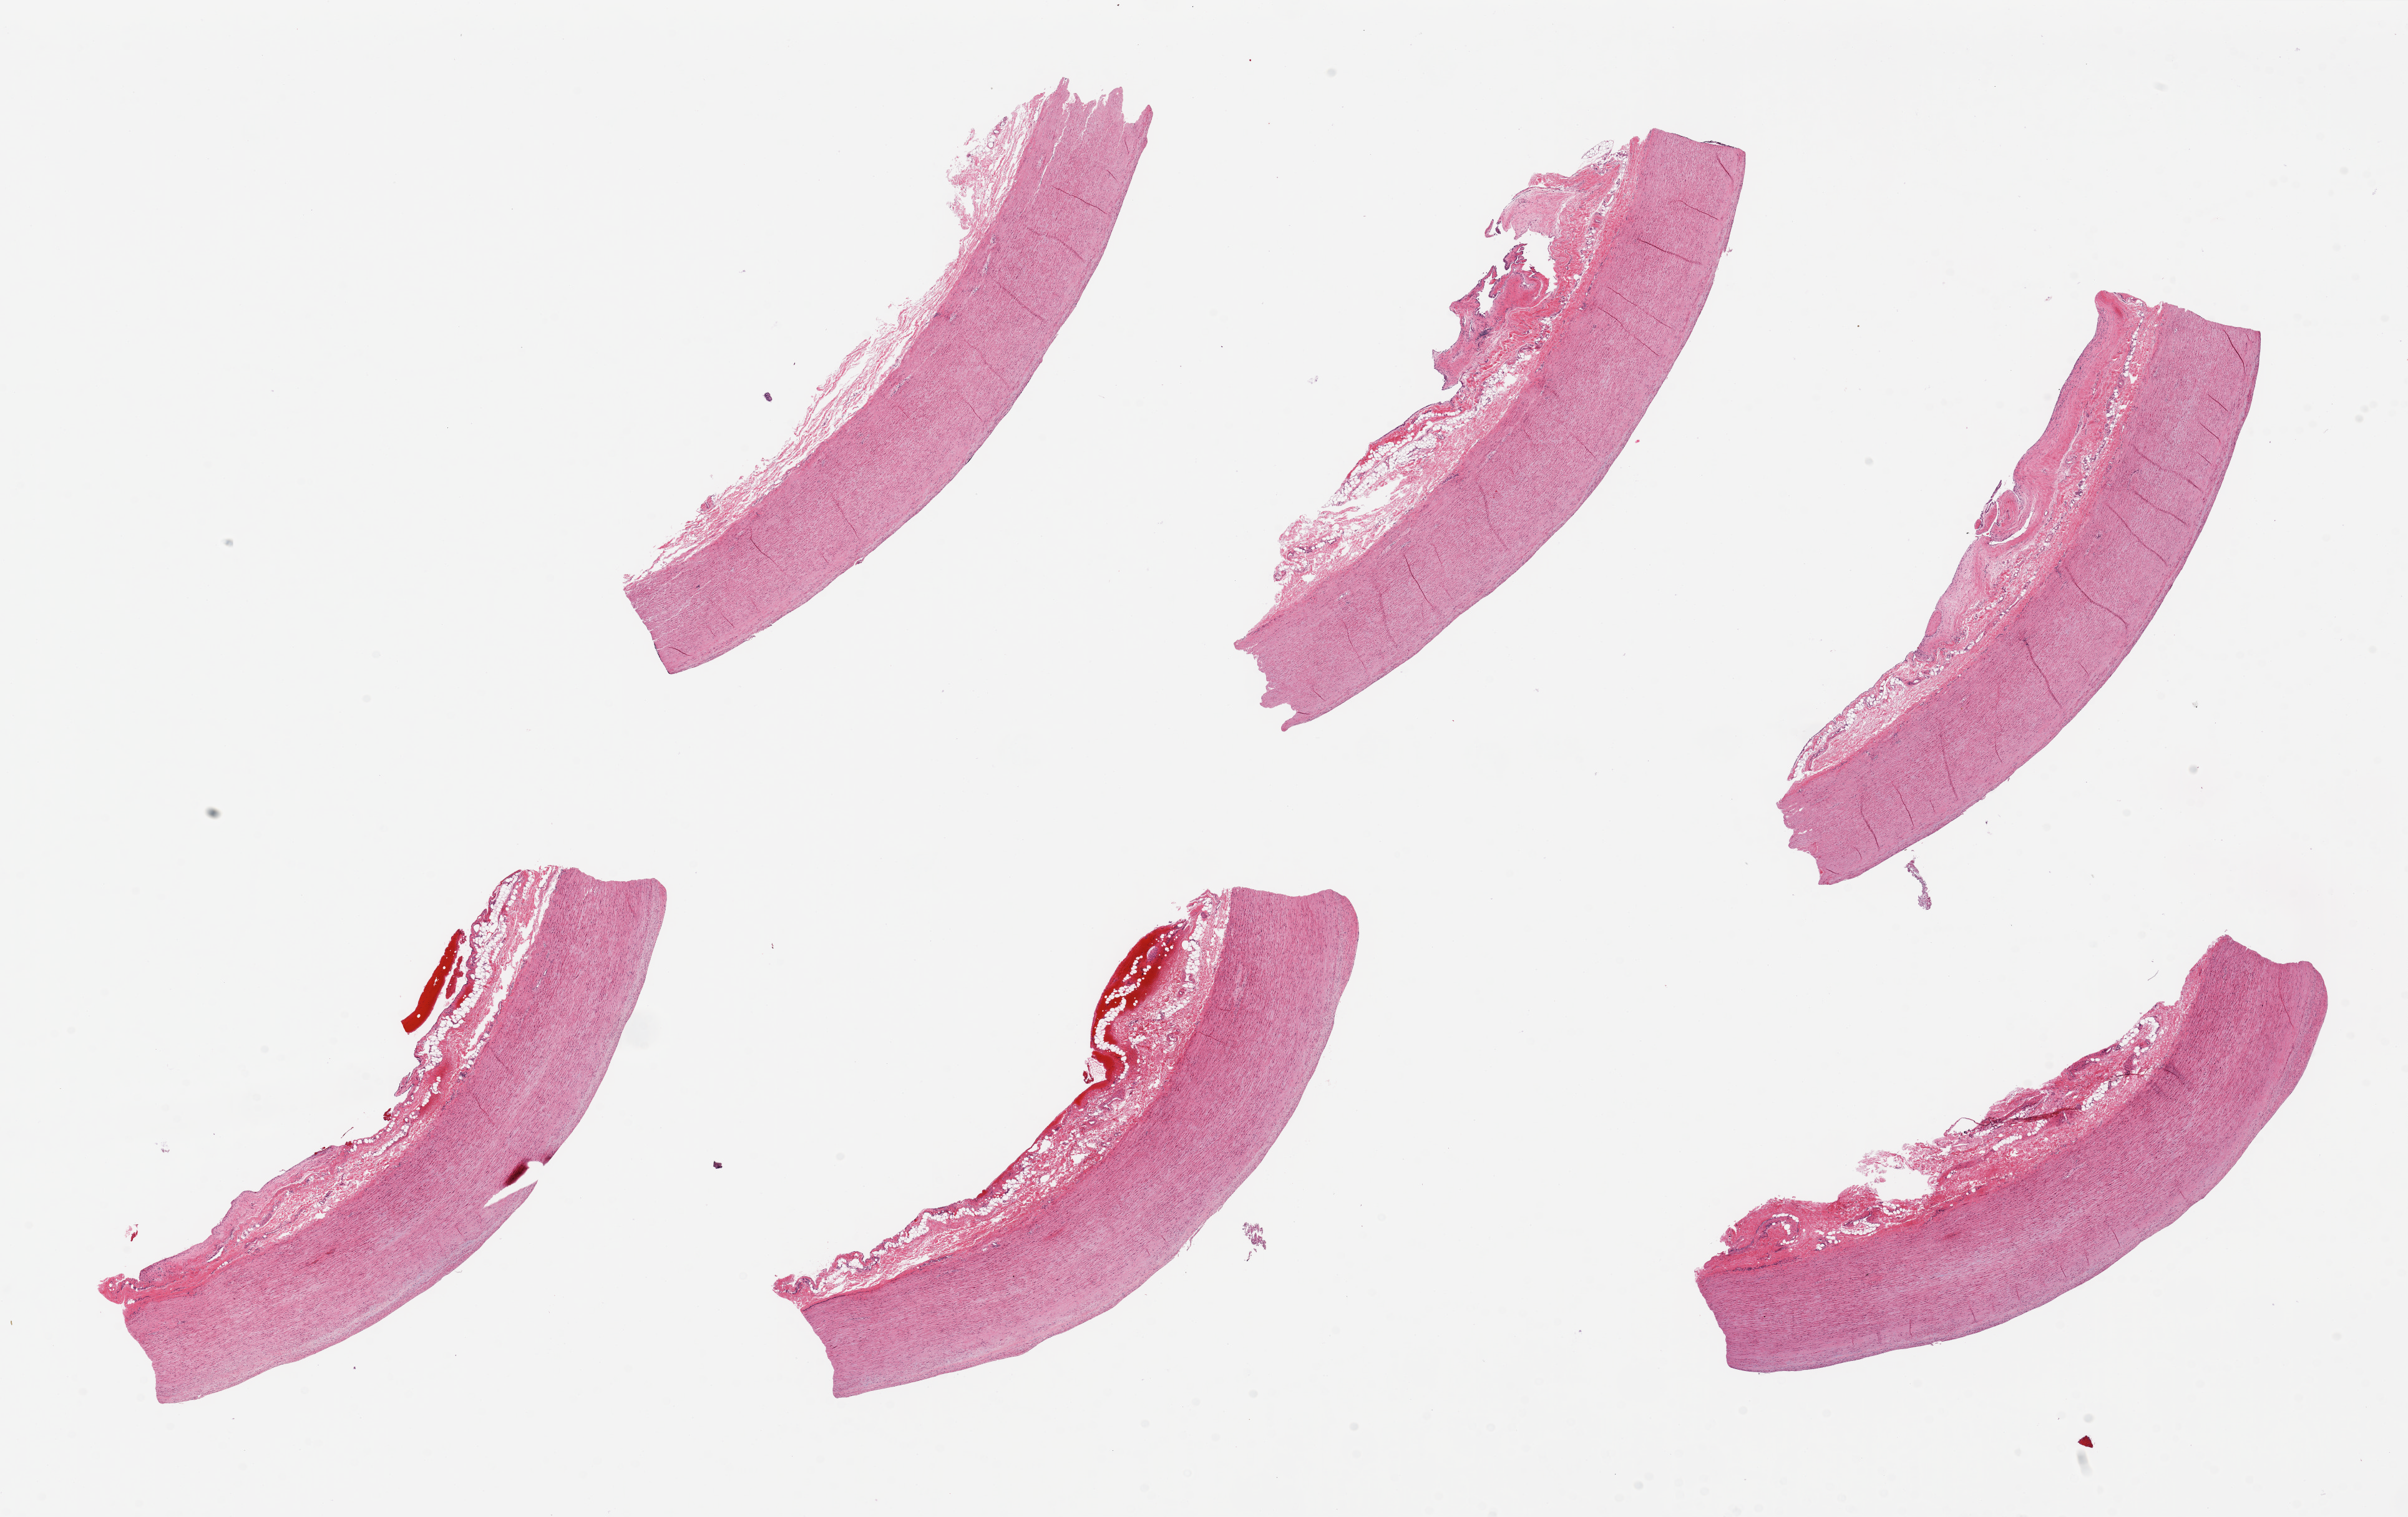
H&E whole-slide image, brightfield — a low-resolution overview of the entire scanned area, about 30.5 x 19.2 mm (from a 20x scan), PAXgene-fixed, paraffin-embedded tissue, target tissue: aorta, donor tissue sample.
Review note (as recorded): 6 pieces ~9x2mm, ~303% thickness is serosa/vasa vasorum; imtmia/media.